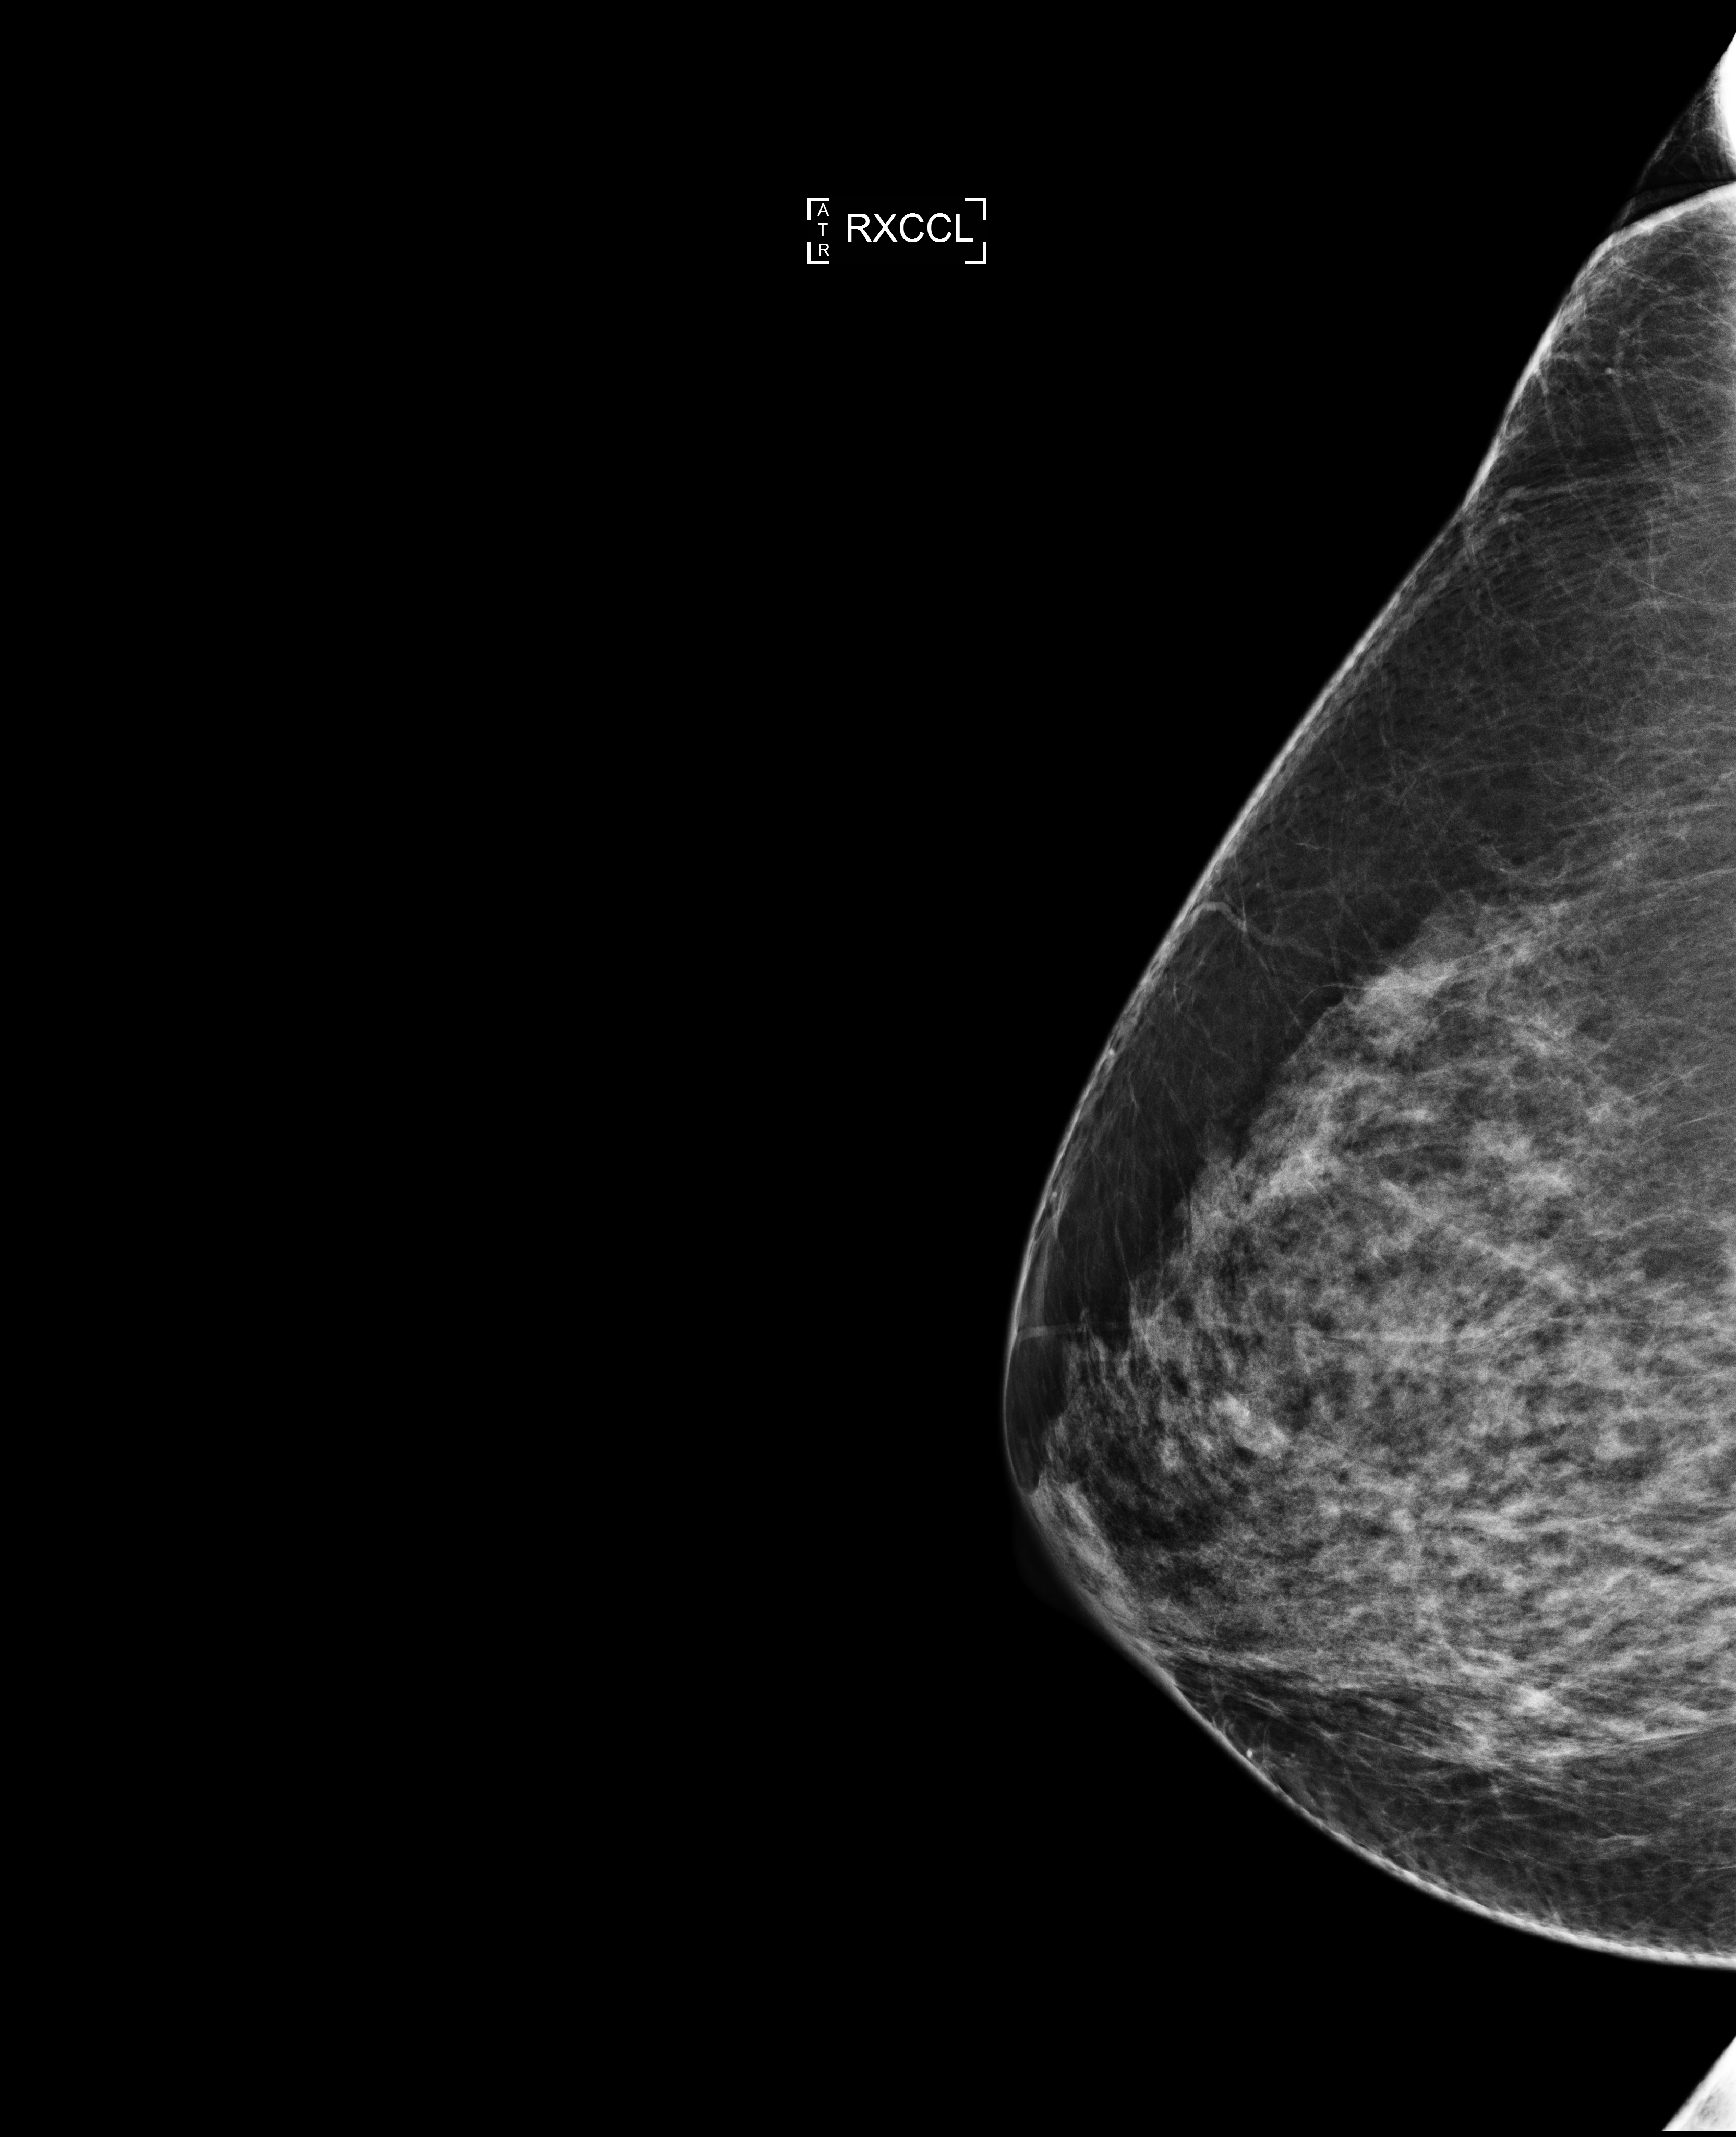
Annual screening mammography examination, compressed breast thickness 80 mm. Female patient, age 53 years.
Image type: full-field digital mammogram. Breast: right. Projection: laterally exaggerated craniocaudal (XCCL) view.